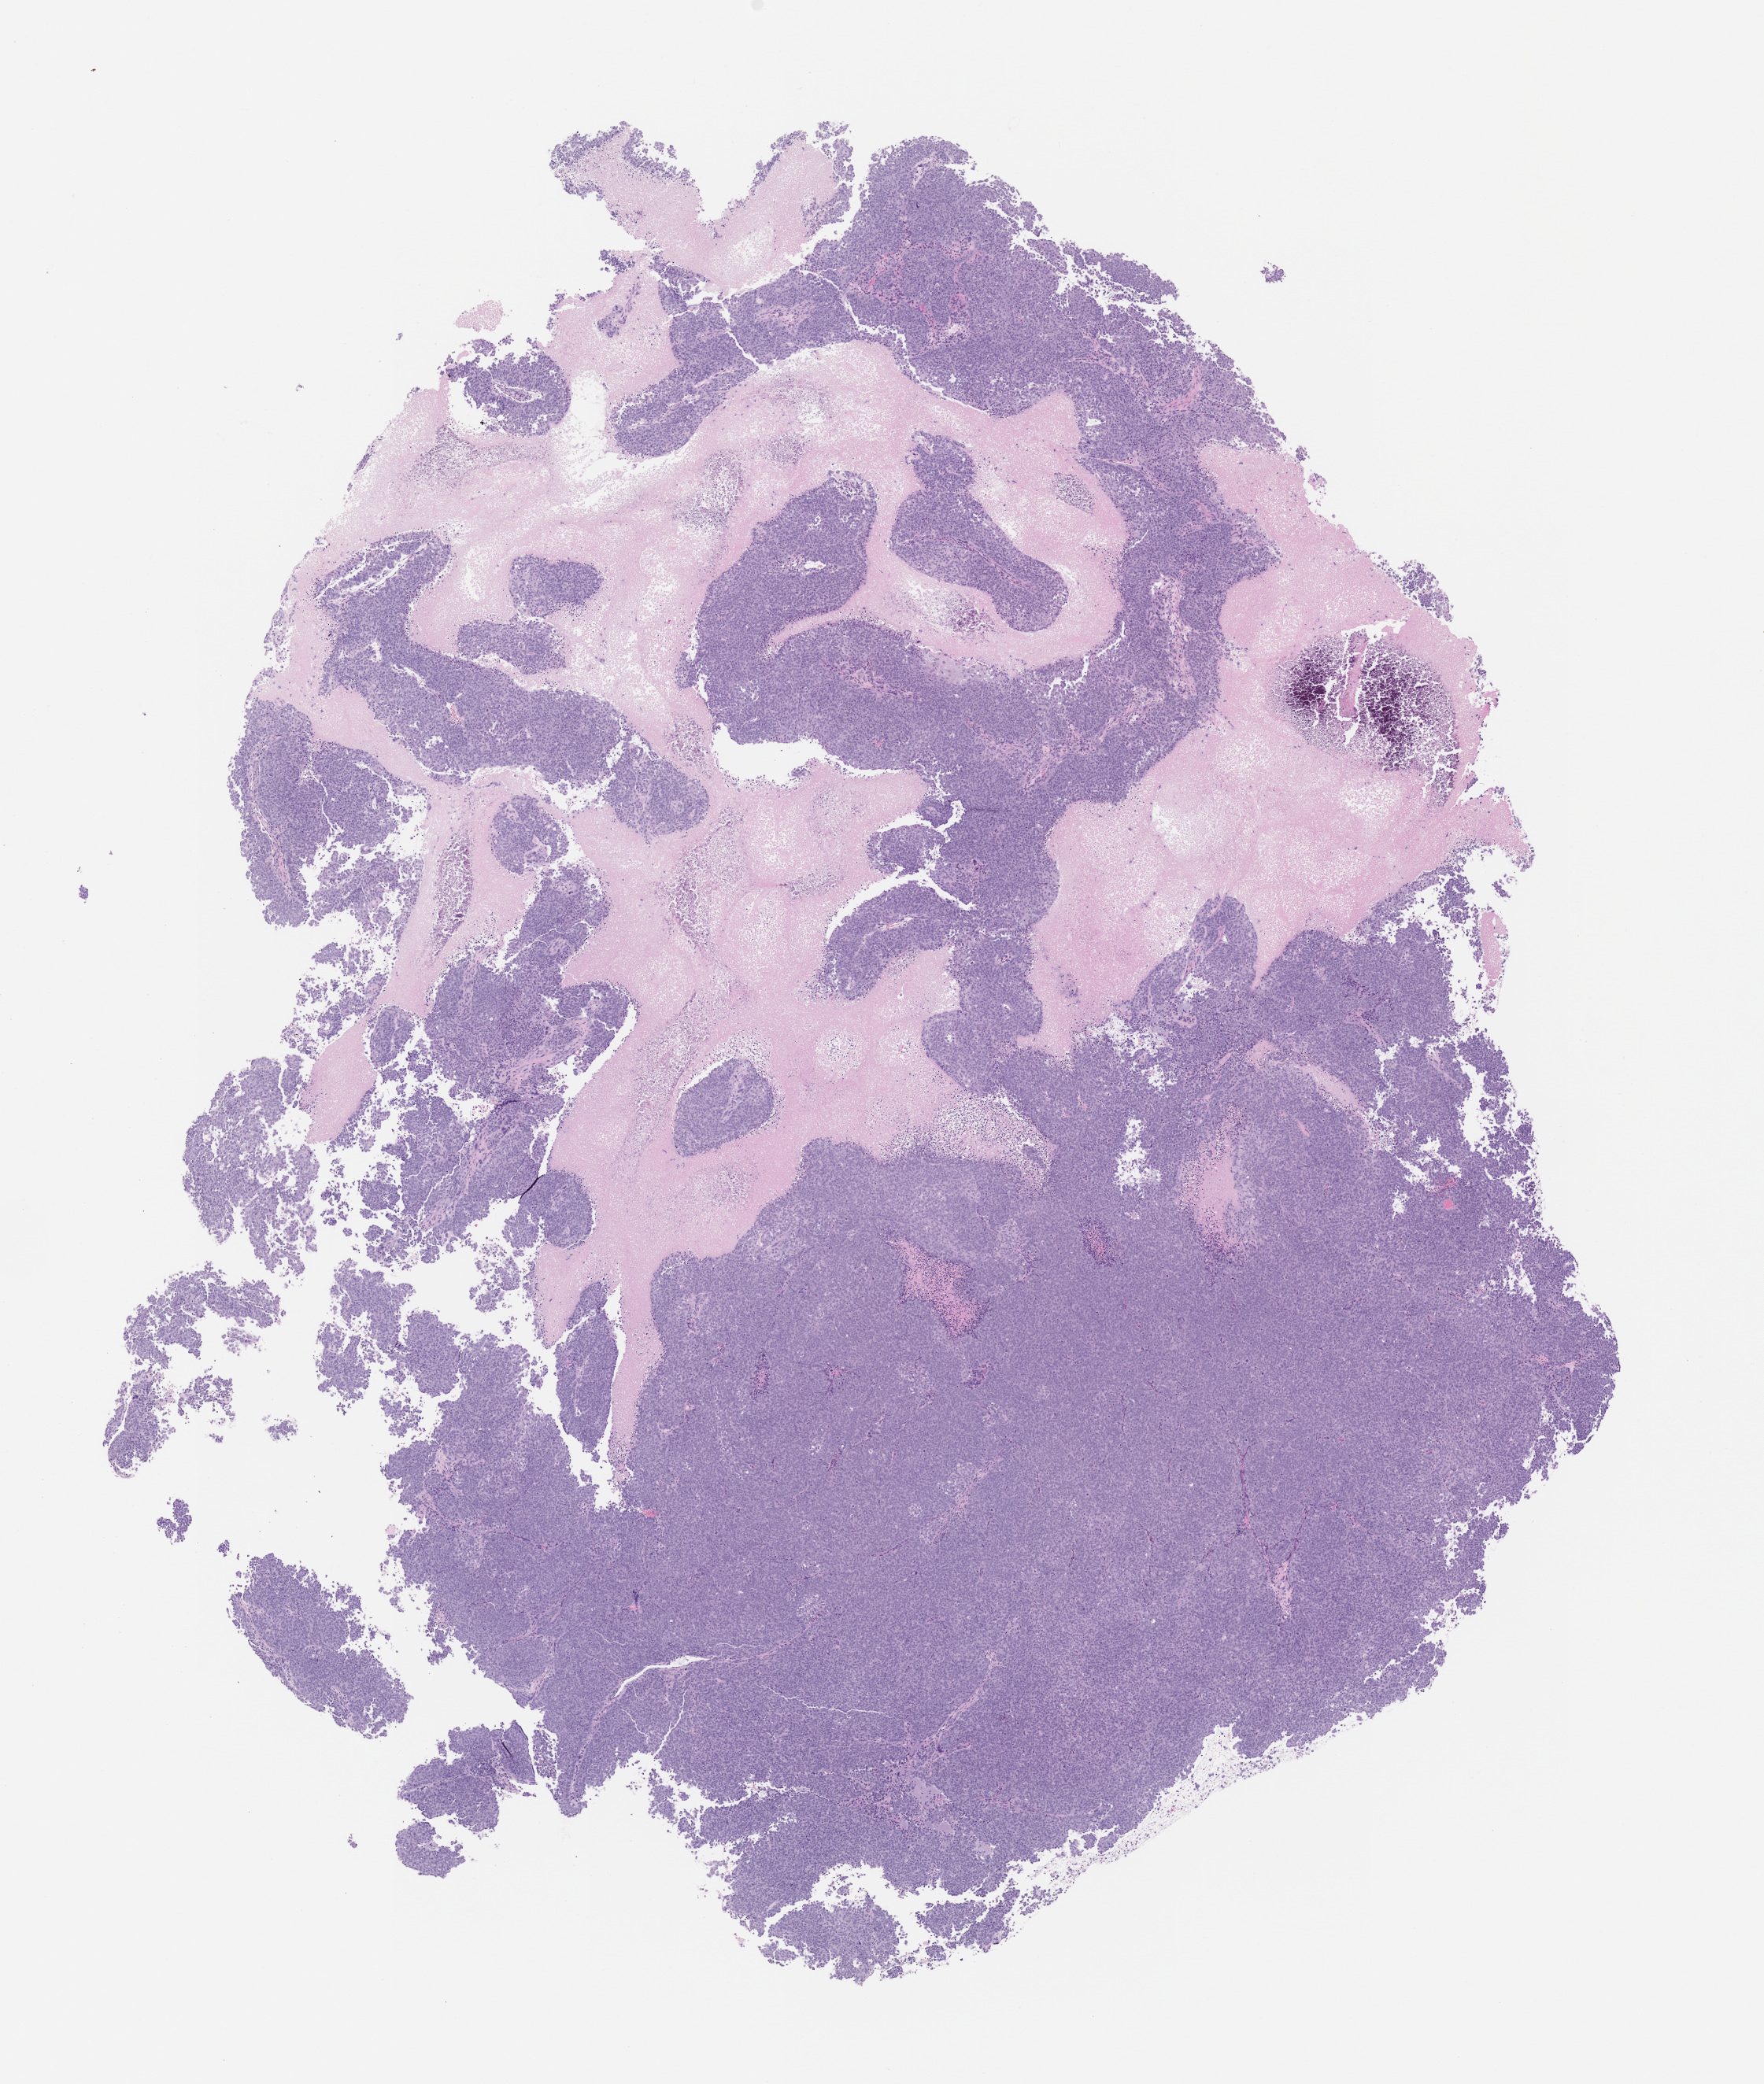
Whole-slide image, hematoxylin and eosin (H&E): patient-derived xenograft (human tumor grown in a mouse), passage 0 — whole scanned area (about 9.0 x 10.6 mm) shown as a low-resolution overview, formalin-fixed, paraffin-embedded (FFPE) tissue, tumor site category: cervix.
* originating patient diagnosis: Cervical Adenocarcinoma